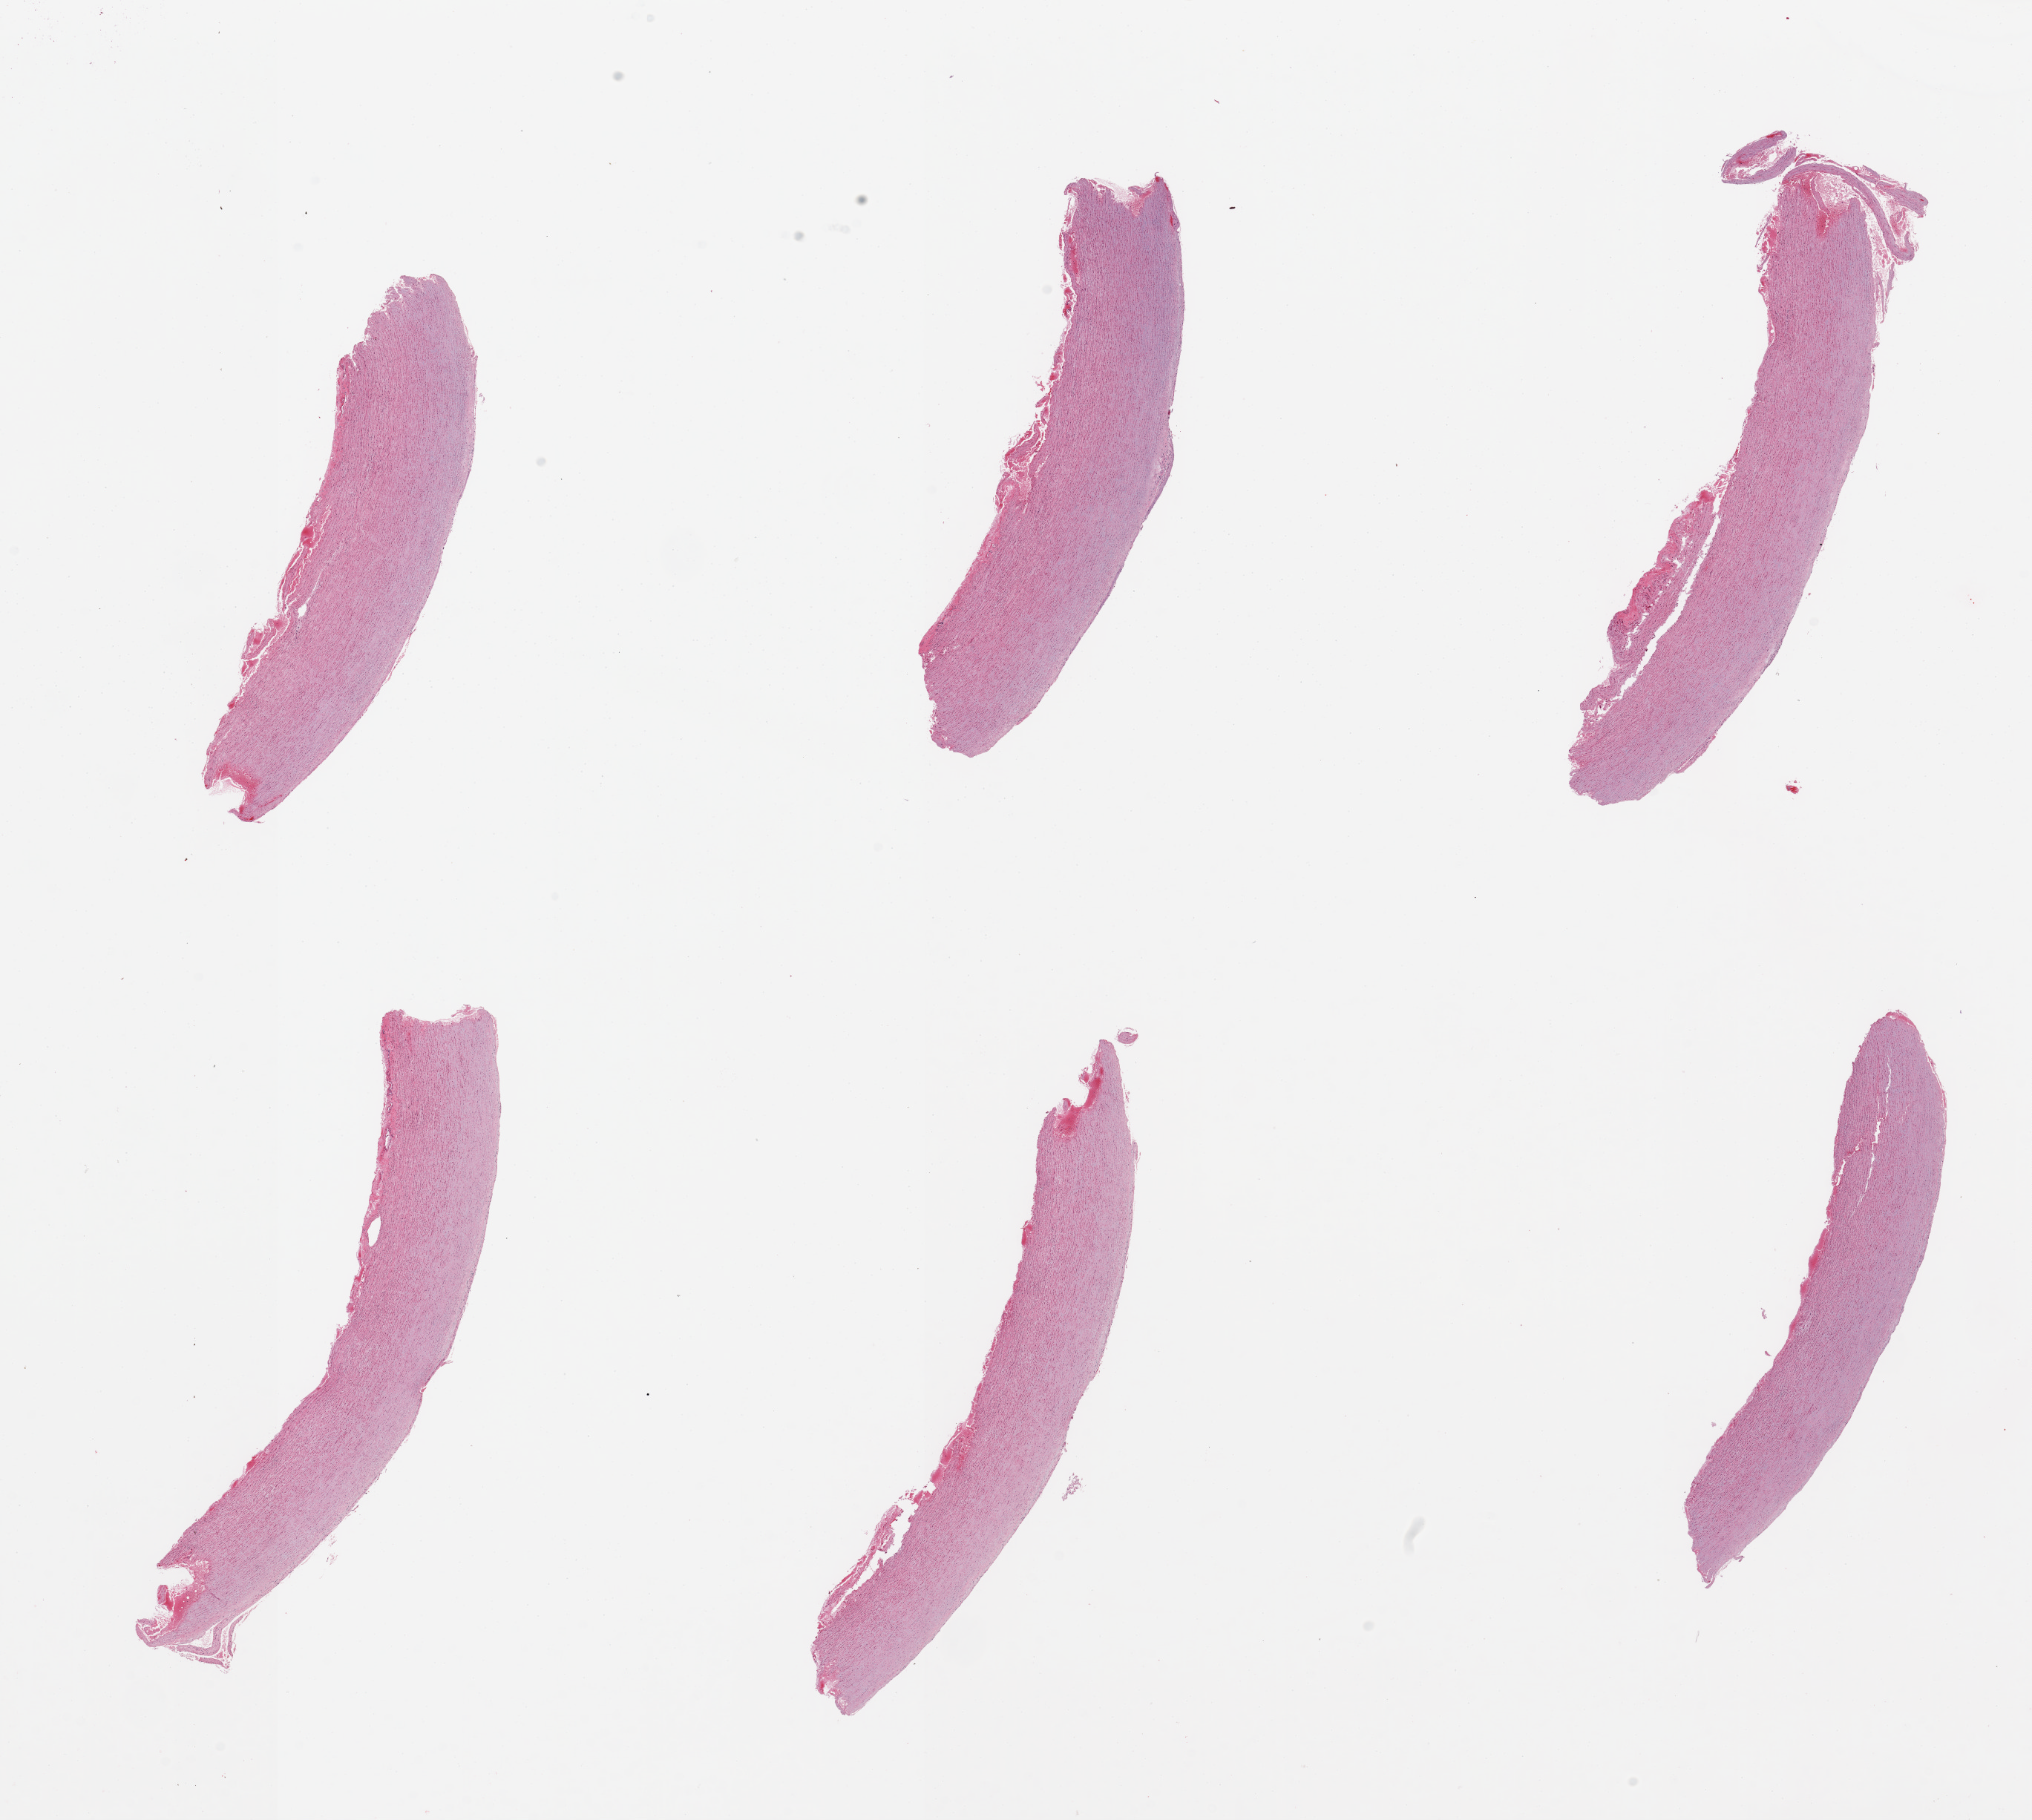
Digitized hematoxylin and eosin (H&E)-stained section — low-resolution overview of the scanned area, about 21.7 x 19.4 mm (from a 20x scan), PAXgene-fixed, paraffin-embedded tissue, sampled site (target tissue): aorta, donor tissue sample. Male donor.
- pathologist's review note for this sample: 6 pieces; mild plaque formation; well trimmed